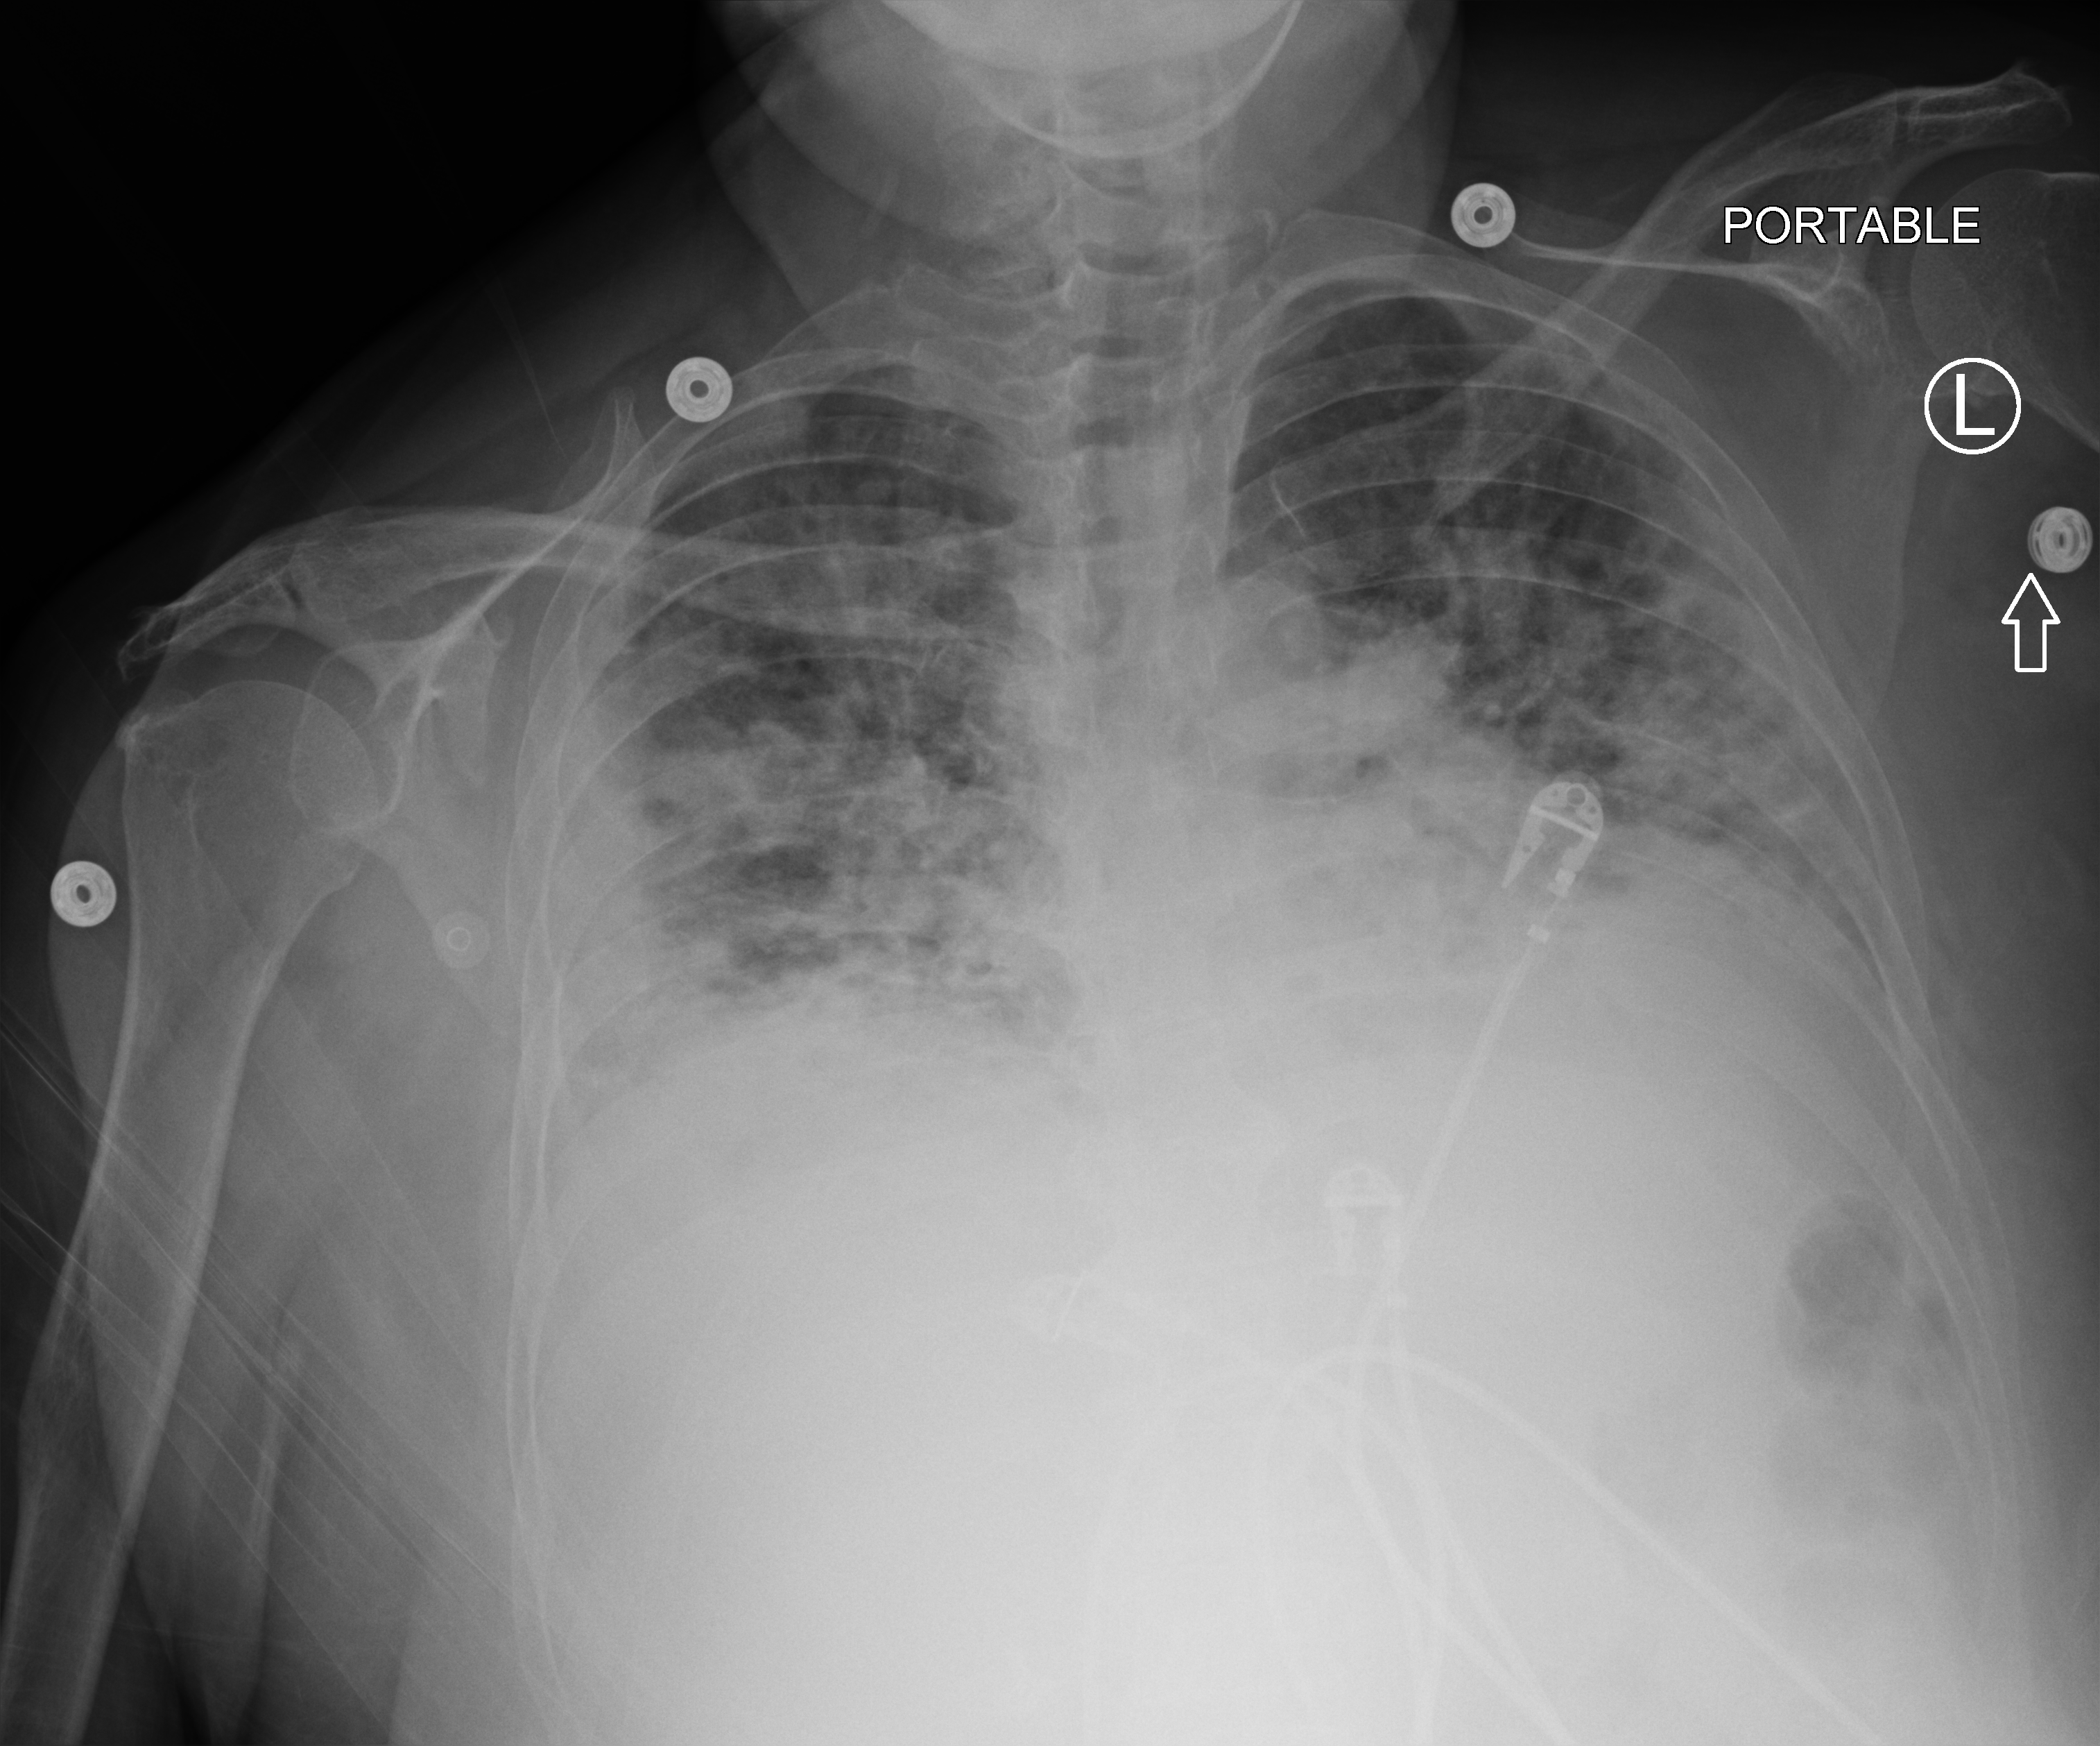
Portable chest radiograph, anteroposterior (AP) projection. Patient hospitalised with COVID-19; female, aged 18–59 years.
From the hospital-stay record, not from the radiograph (when in the stay this image was taken is not recorded): admitted to intensive care during this hospital stay: yes.